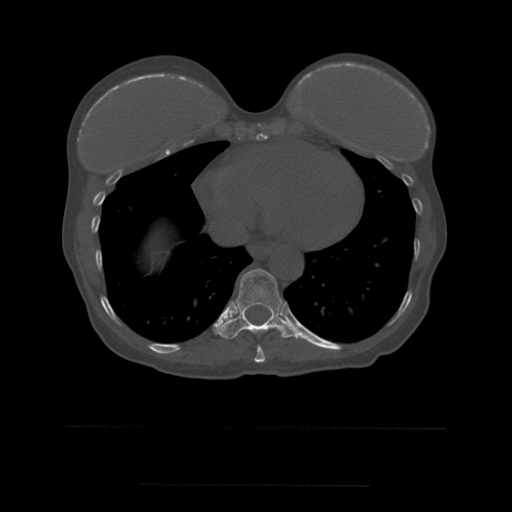
CT including the spine, one axial slice; position 306 of 544 along the scan axis; bone window (W 1800 / L 400 HU); 1.25 mm slice thickness; 512 × 512 image matrix. Patient age 58 years. Case-level facts recorded for this patient, not image findings: primary cancer: lung.
Outlined on this slice (semi-automatically segmented with operator editing):
- T10 vertebra: box from (x=215, y=269) to (x=297, y=339) px
- T9 vertebra: (x=254, y=346)–(x=266, y=363)